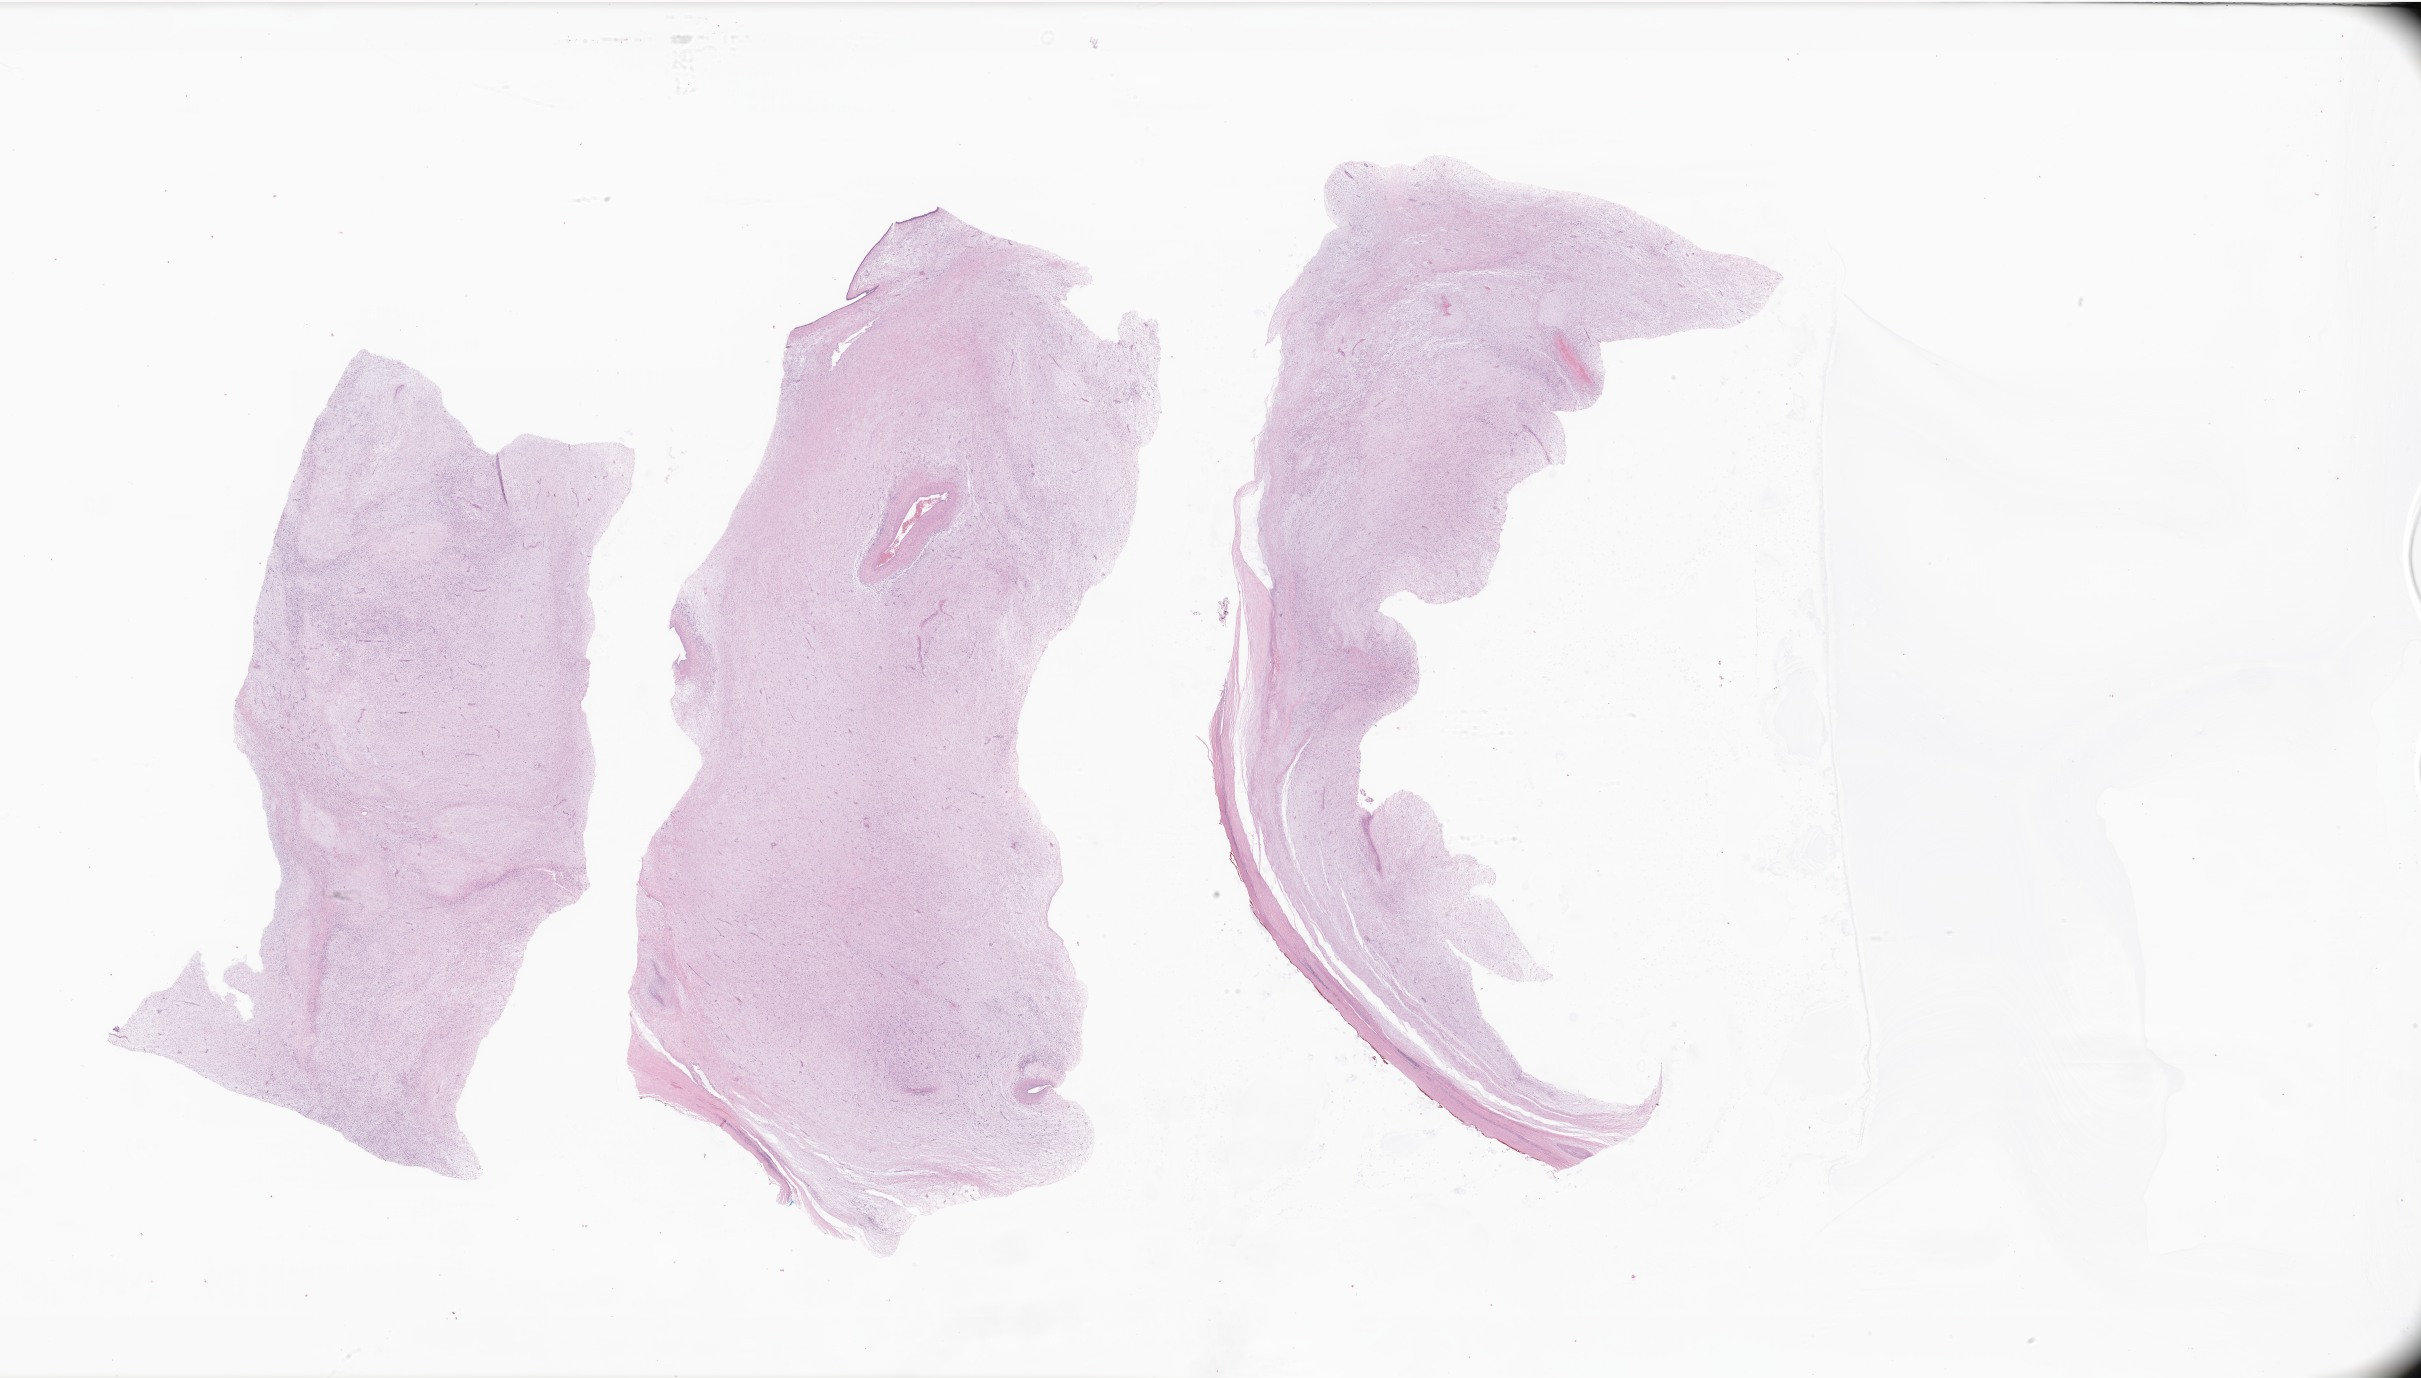
H&E whole-slide image of tumor tissue from the mediastinum — a low-resolution overview of the entire scanned area, about 40.8 x 23.2 mm; FFPE section. Patient: female, age 171 months (14 years 3 months).
Recorded diagnosis: Embryonal rhabdomyosarcoma, NOS.